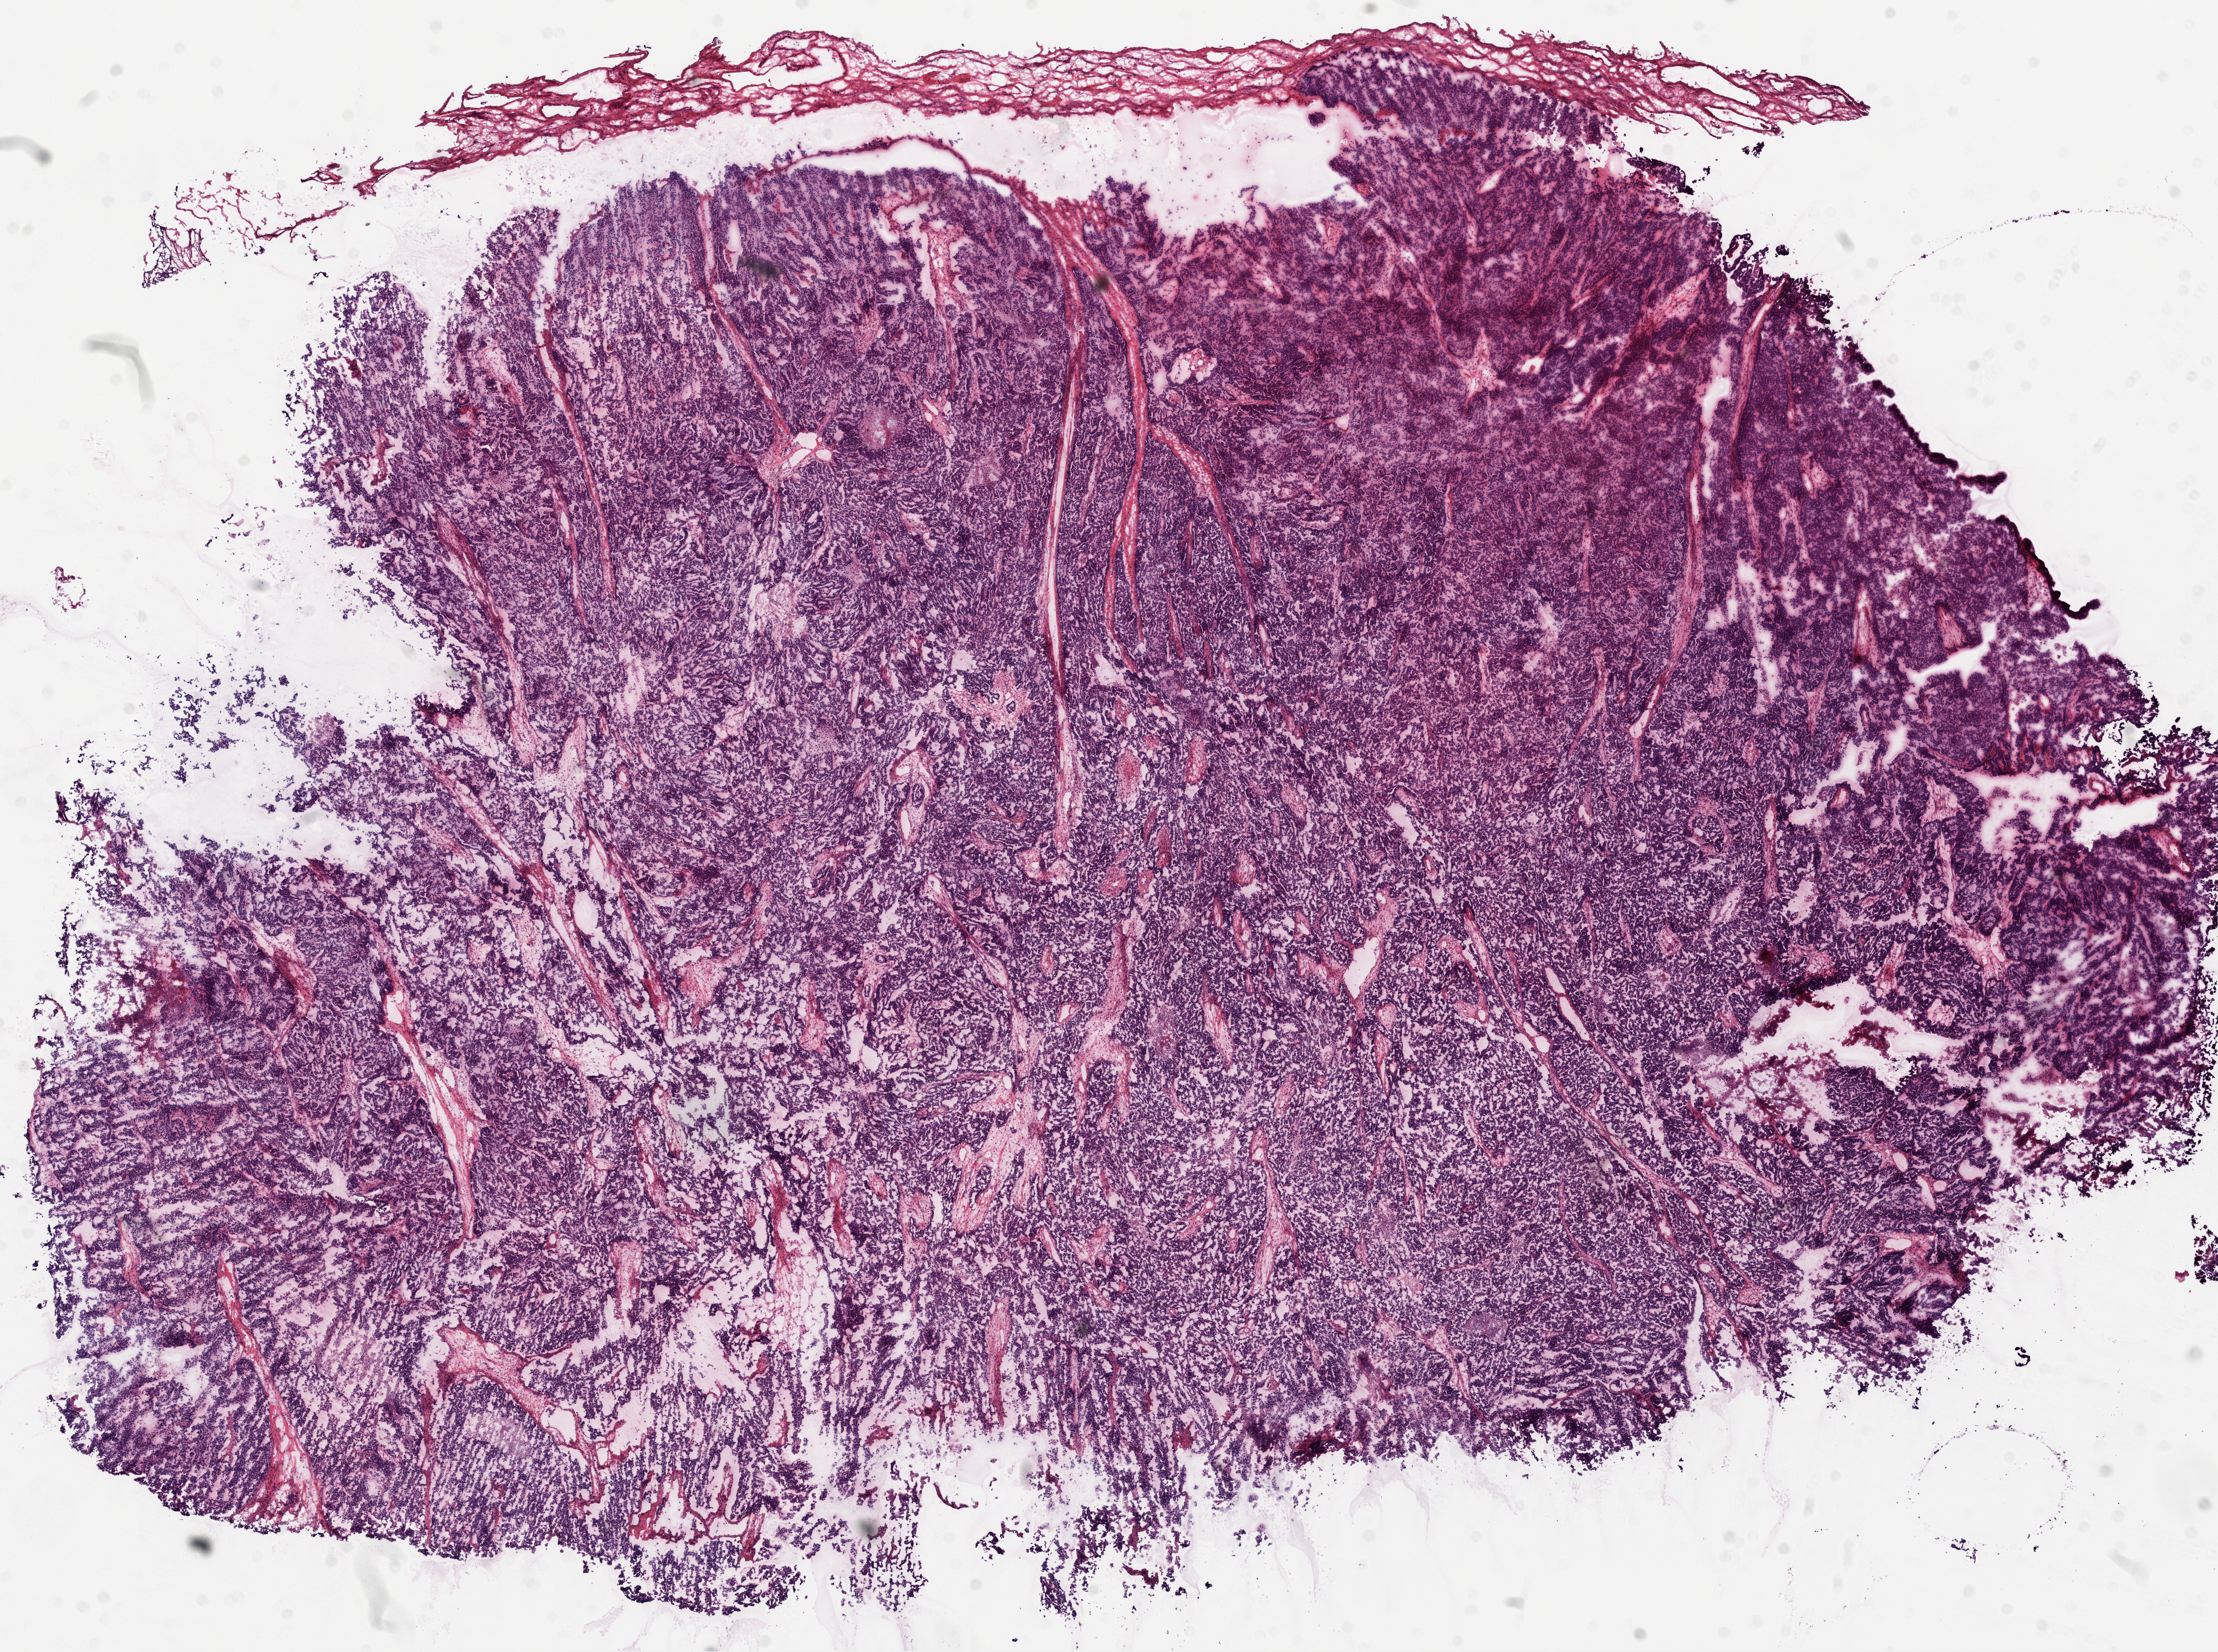
Whole-slide histology image, H&E, a low-resolution overview of the entire scanned area, about 16.0 x 12.0 mm (acquisition: 20x scan). Frozen section. Ovary, primary tumour sample. Female patient; age at initial diagnosis 70 years. Histologic grade: G2 (moderately differentiated). Pathologist review of this section (percent, as recorded): tumour cells 95%, tumour nuclei 98%, normal cells 5%, stromal cells 0%, necrosis 2%. Infiltration values recorded for this section: lymphocyte infiltration 50%, neutrophil infiltration 50%.
FIGO stage: IIIC. Diagnosis: Serous cystadenocarcinoma, NOS.